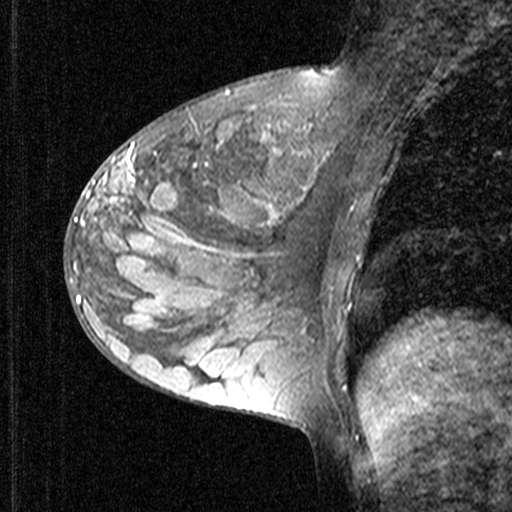
Breast MRI (dynamic contrast-enhanced), one sagittal slice; dynamic contrast-enhanced study with each time point stored as its own series, time point 2 of 3 at this slice position (early post-contrast, ordered by acquisition time); 1.5 T; TE 4.5 ms, TR 11 ms; 3 mm slice thickness; 512 × 512 image matrix, field of view 200 × 200 mm. Female patient, age 27 years. Case-level facts recorded for this patient, not image findings: setting: breast cancer imaged before/during neoadjuvant chemotherapy; receptor status: HR-positive, HER2-negative.
Structures marked on this image (semi-automatically segmented with operator editing):
- analysis volume of interest (the breast-tissue region the enhancement analysis was run in; not a lesion): bounding box [x1, y1, x2, y2] px = [68, 146, 165, 239]
- tumour enhancement mask (voxels above the 90 % enhancement threshold inside the analysis volume of interest): [74, 146, 133, 225]